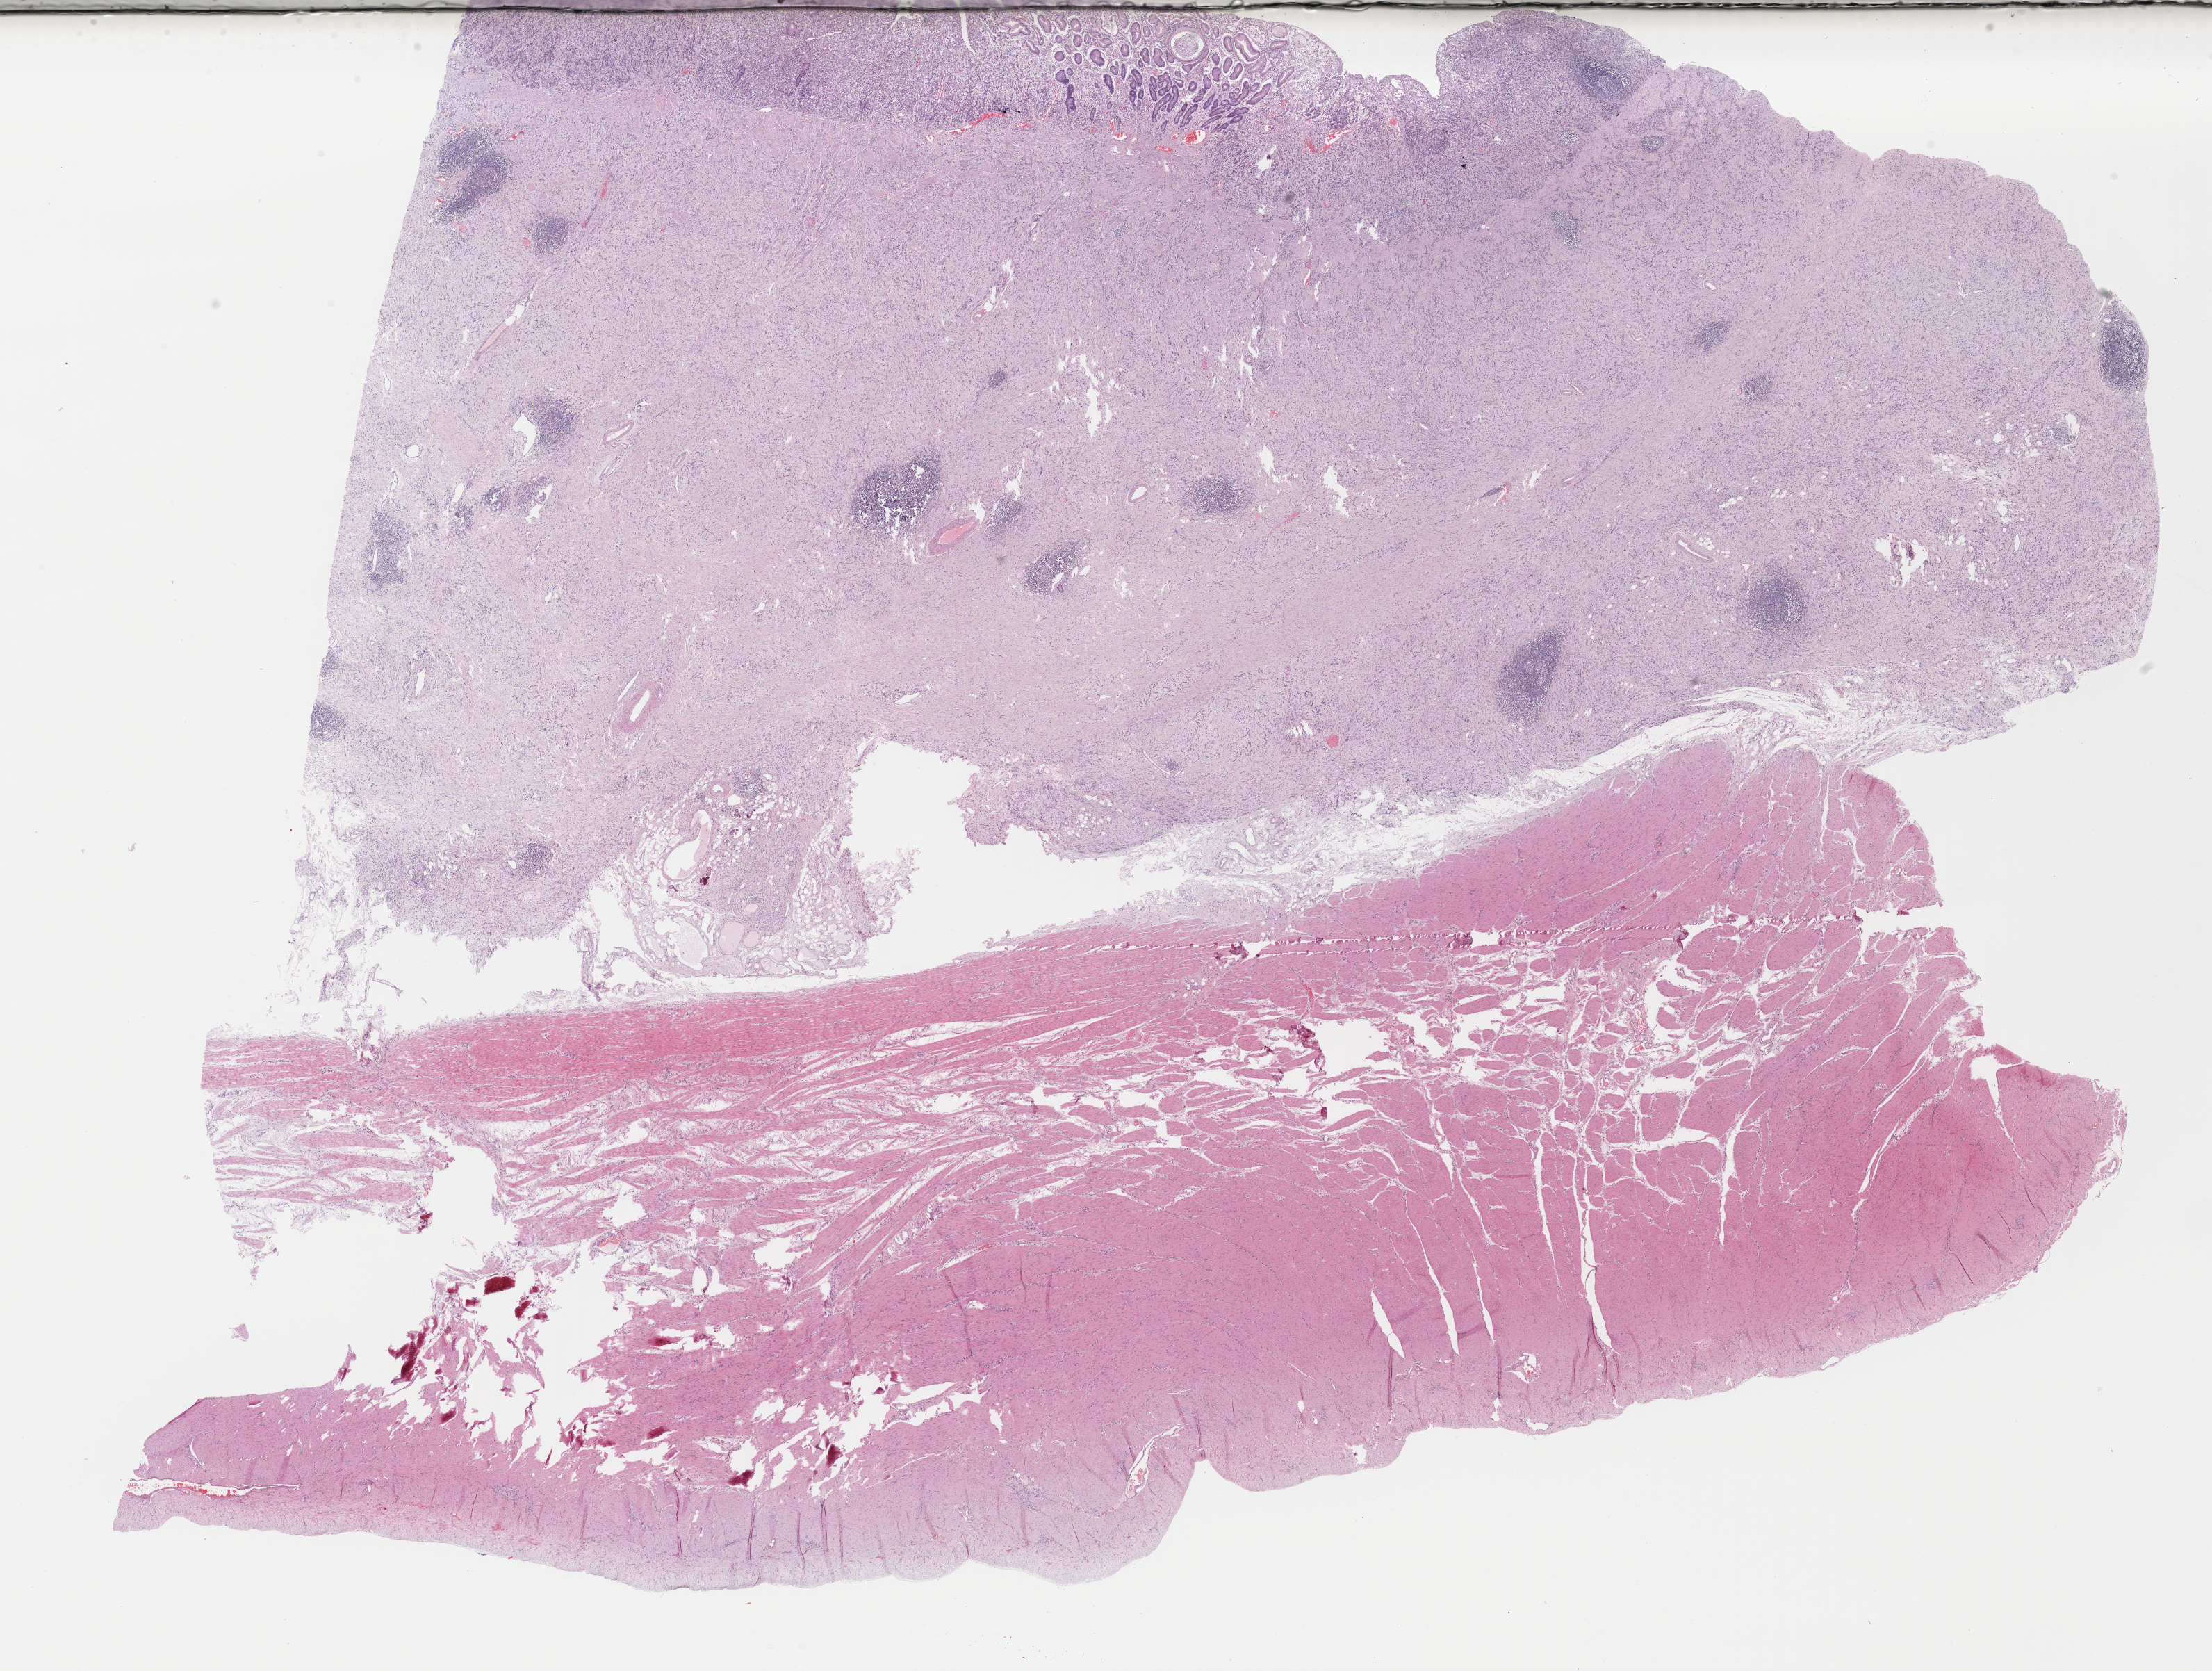
Whole-slide histology image, H&E — whole scanned area (about 25.1 x 19.0 mm) shown as a low-resolution overview, FFPE section, primary tumour sample from the stomach. Female, age 60 years at initial diagnosis. Histologic grade: G3 (poorly differentiated).
AJCC pathologic stage: IIB (7th edition). Diagnosis: Mucinous adenocarcinoma. Lymph nodes positive (case pathology): 3 of 10 examined.